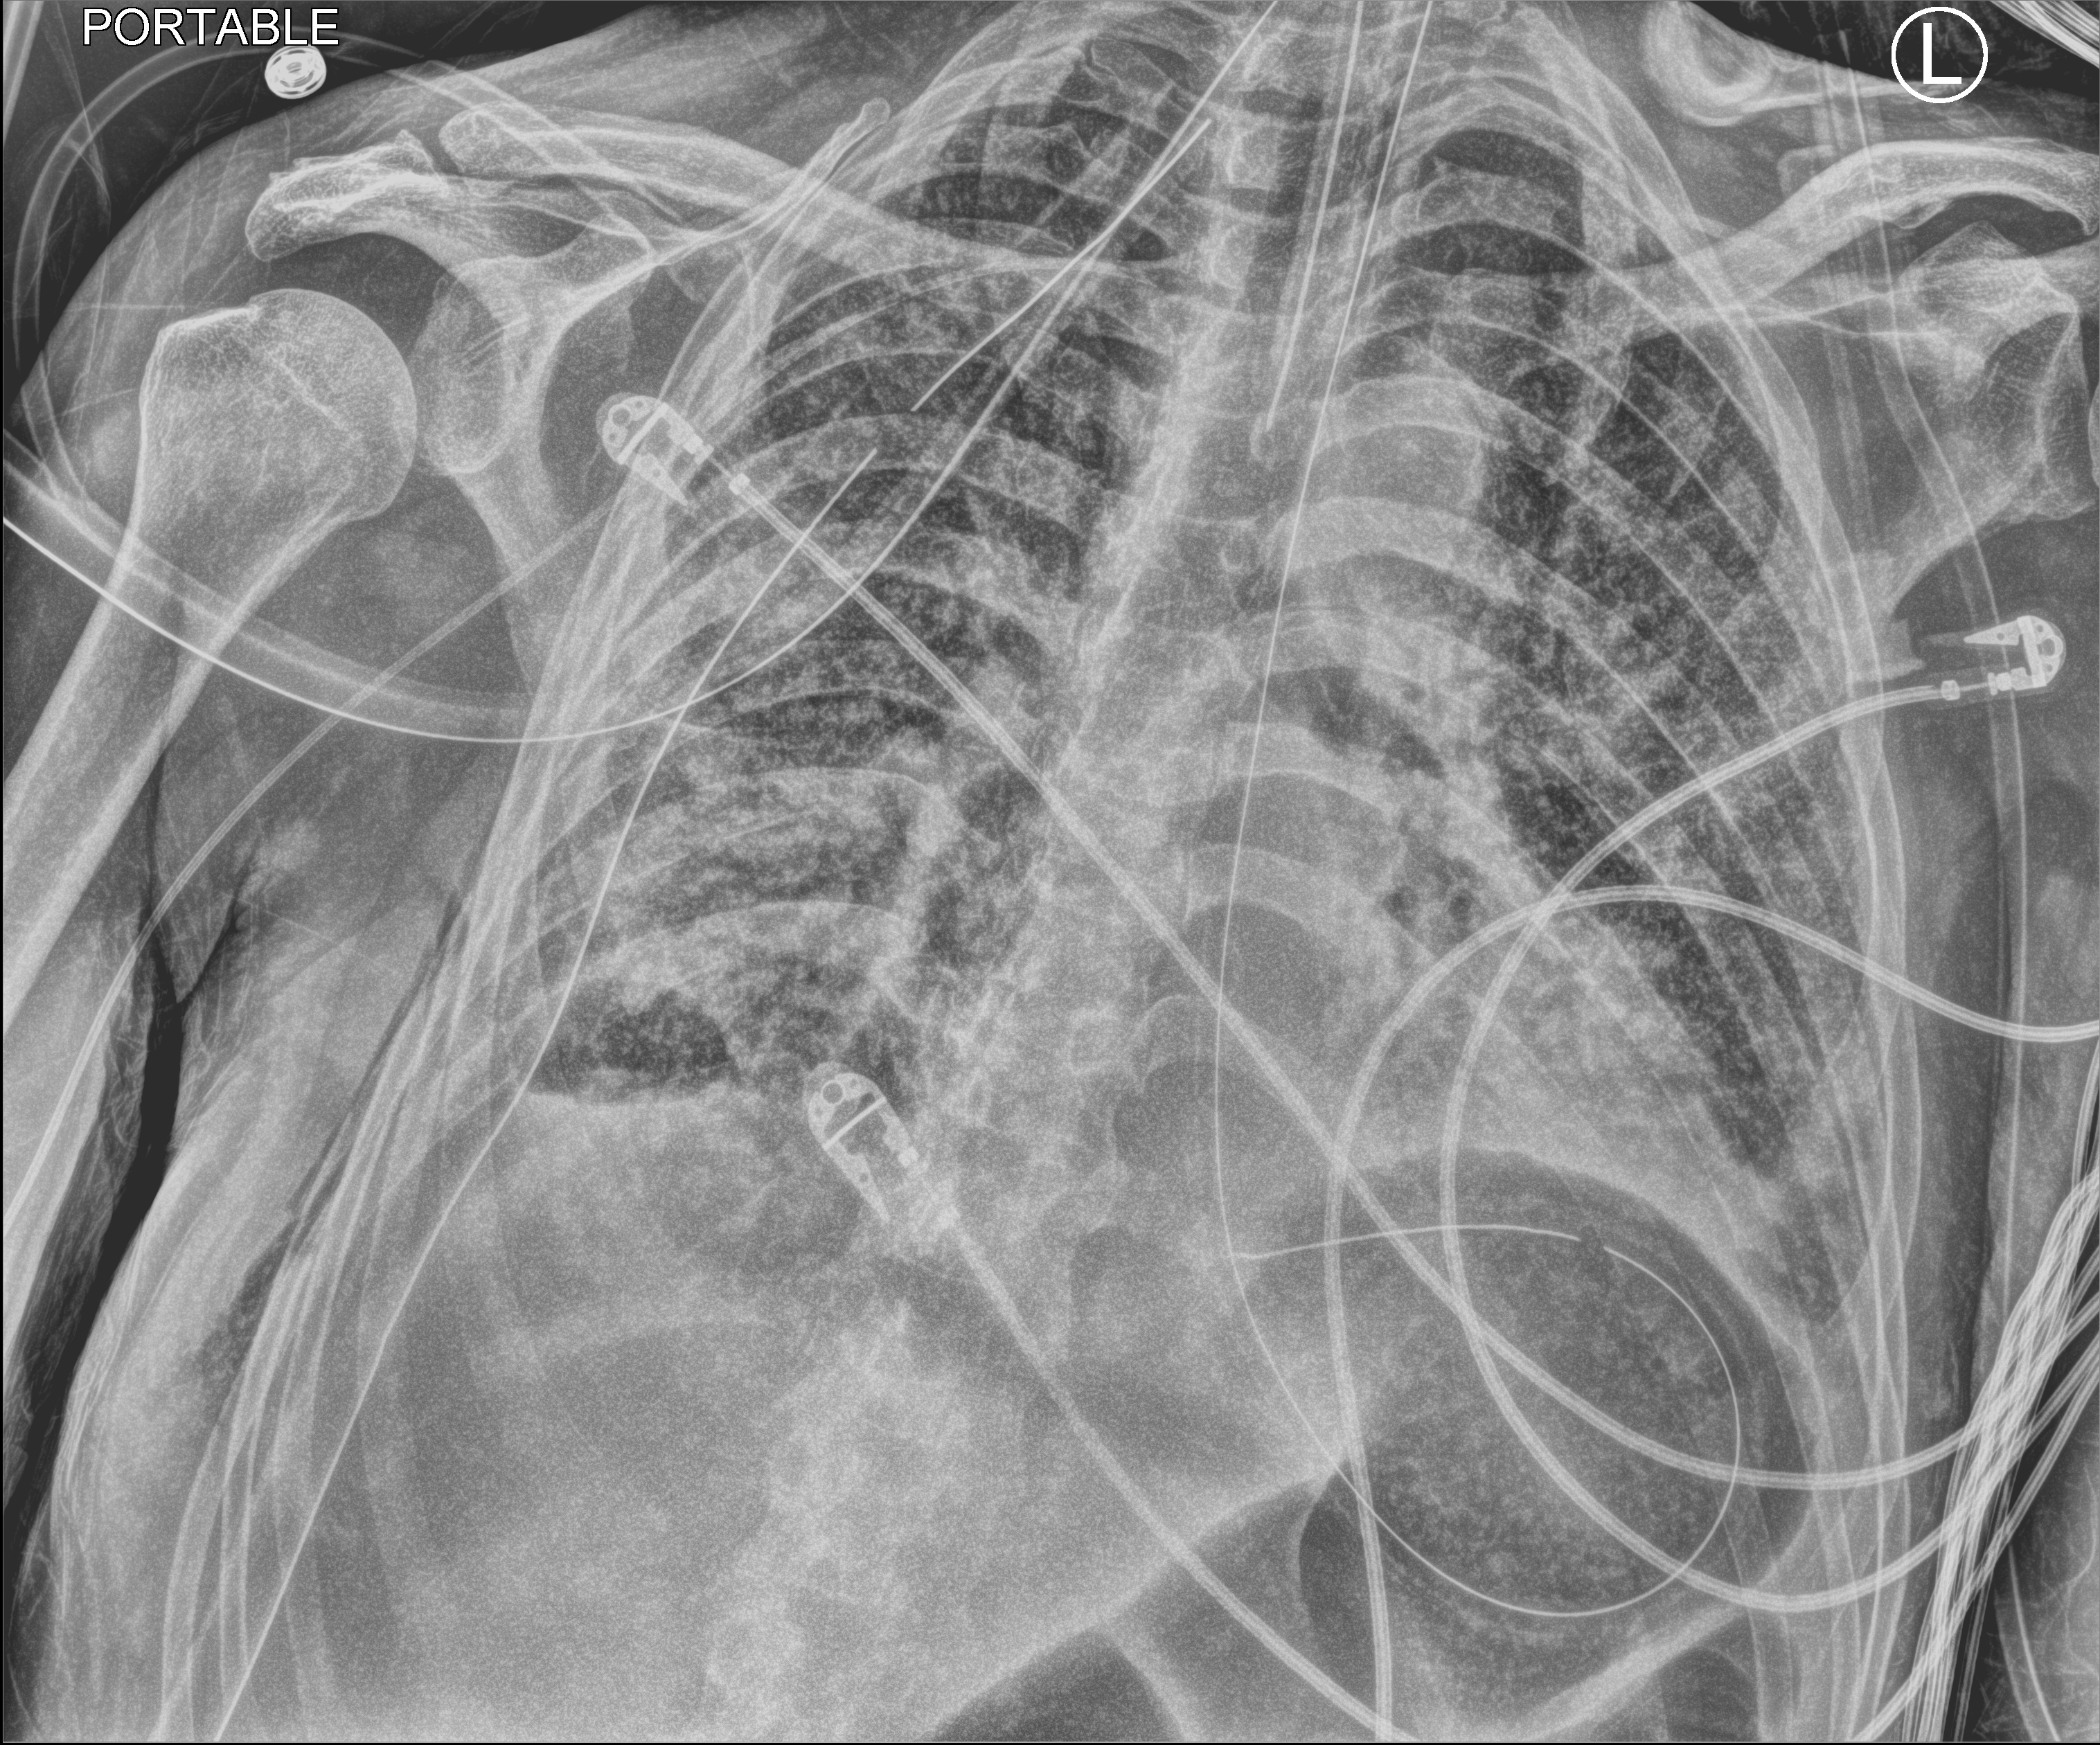
Chest X-ray (portable); anteroposterior (AP) projection. Male patient hospitalised with COVID-19, age 60–74 years.
Hospital-stay facts (about this admission, not read from this image; timing relative to this image not recorded):
- mechanically ventilated during this hospital stay: yes
- diabetes (admission record): yes
- other chronic lung disease (admission record): no